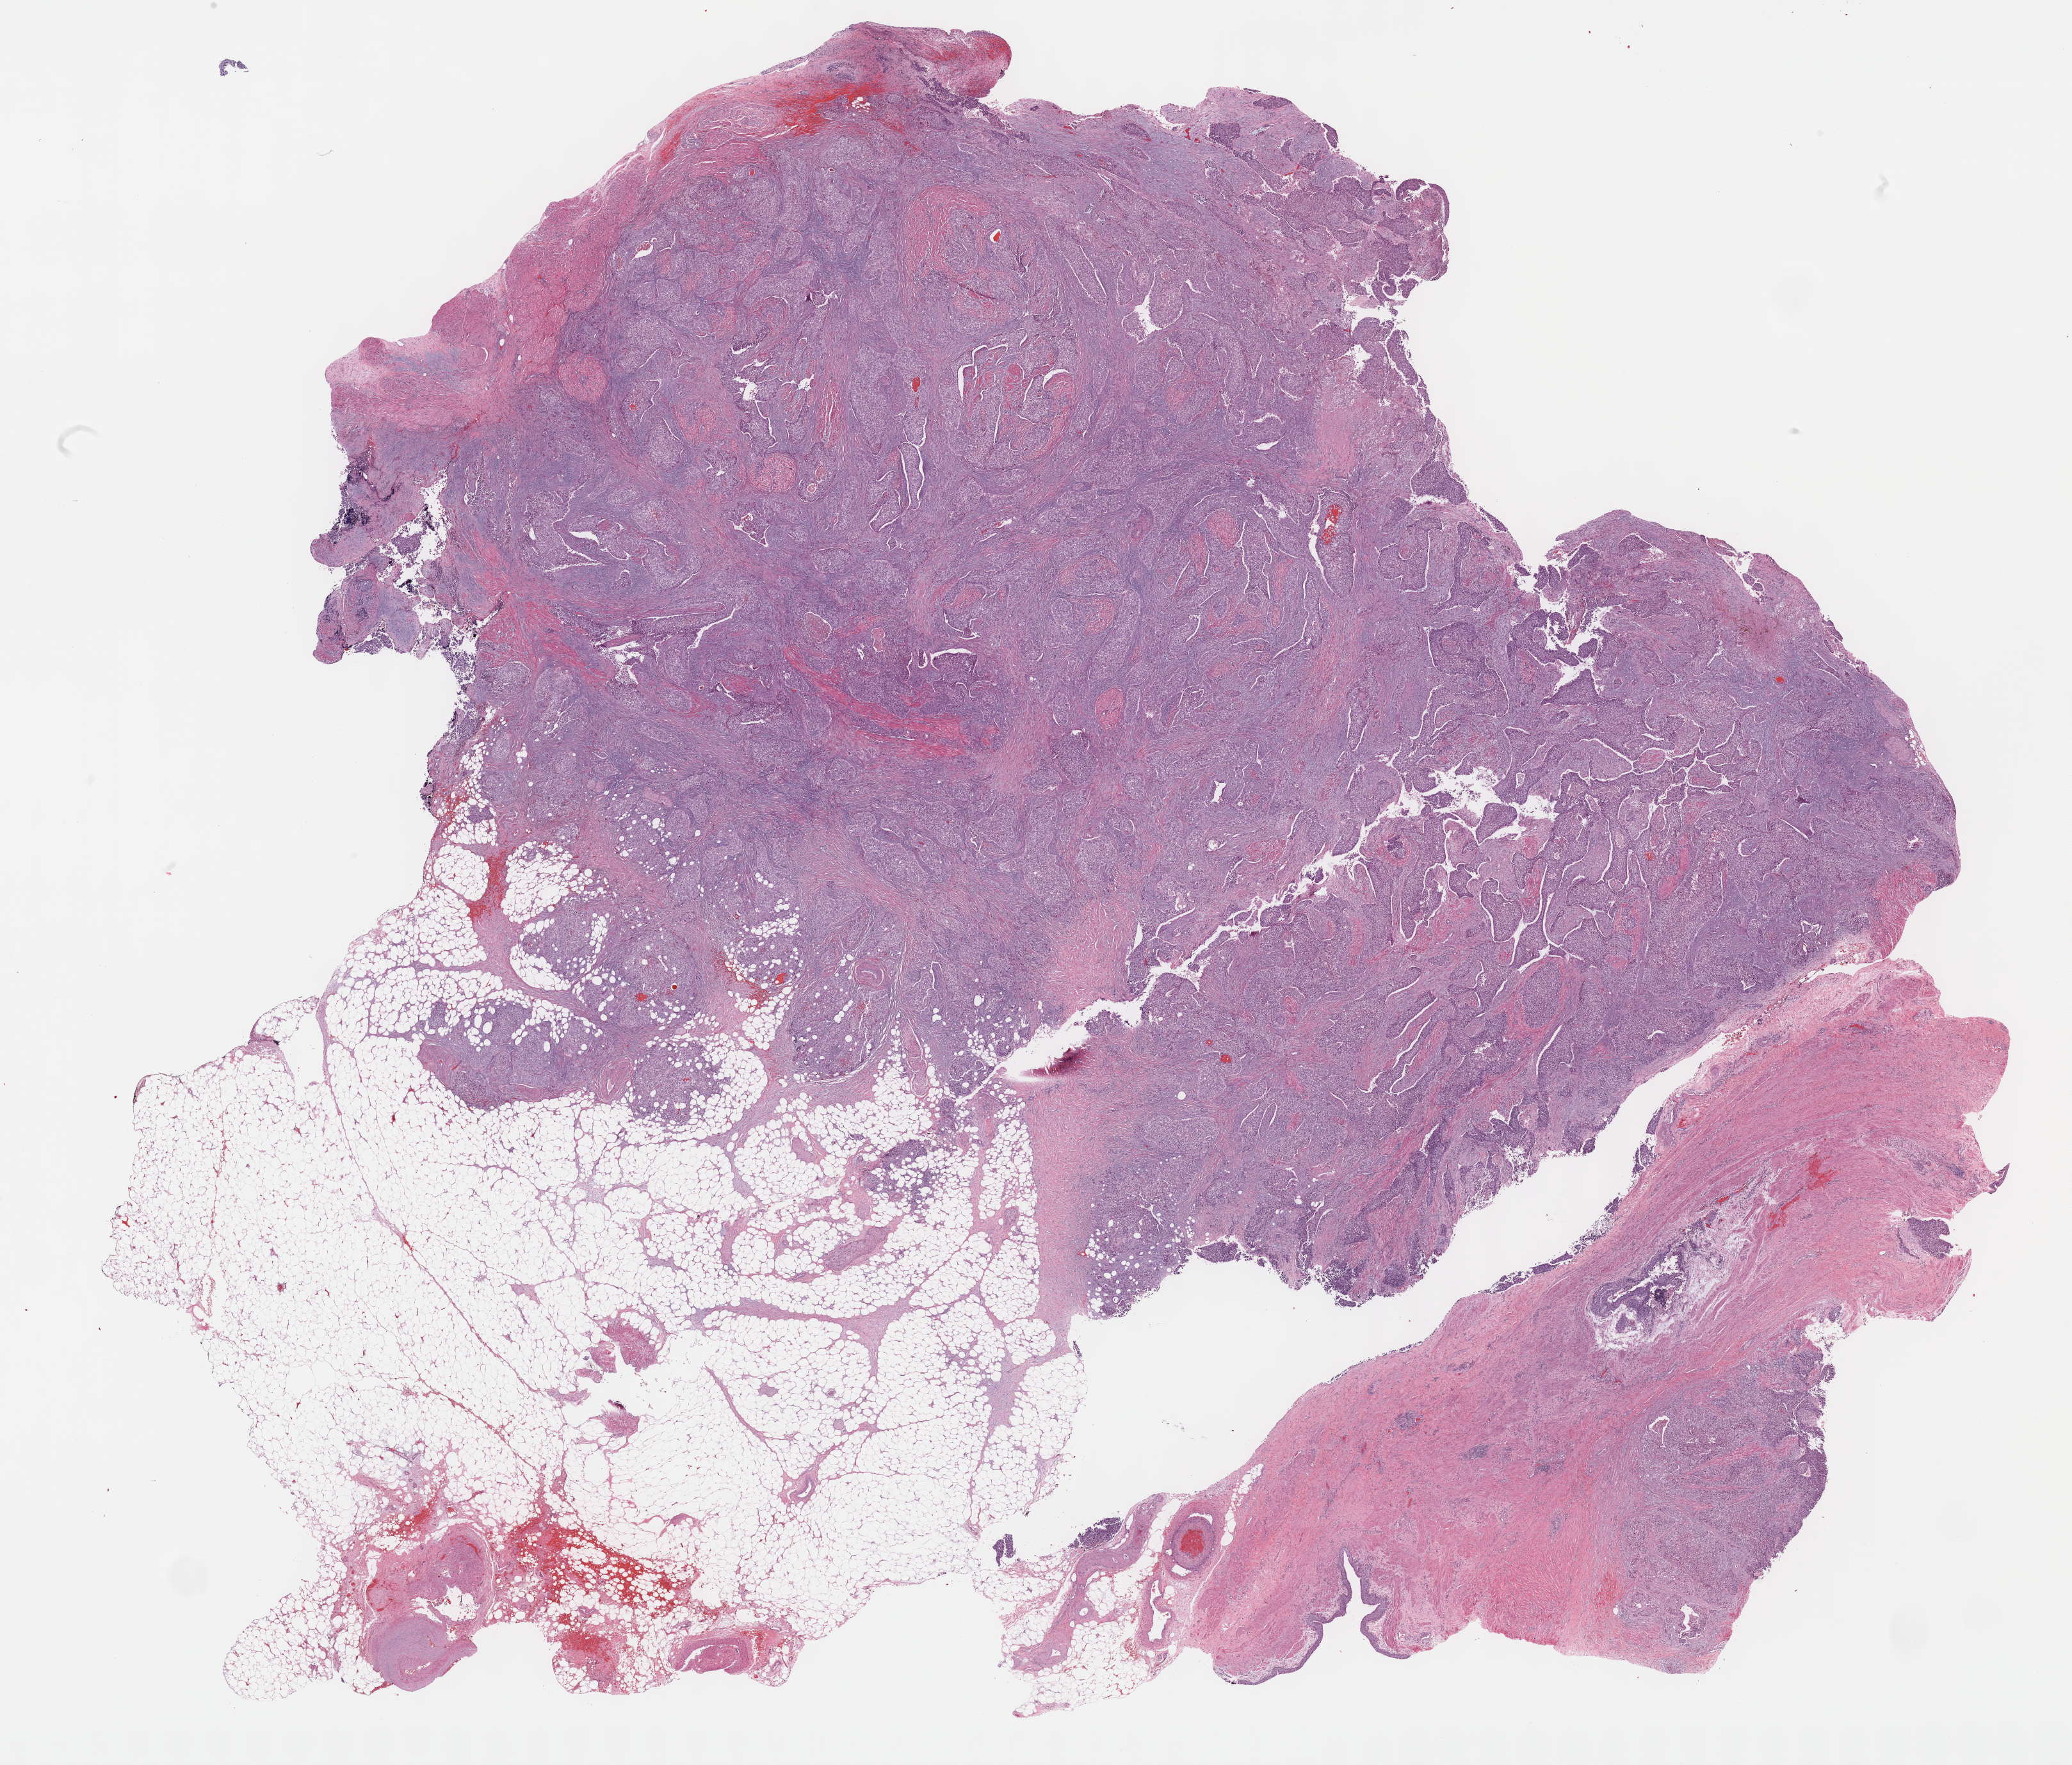
Digitized H&E tissue section (whole slide) — whole scanned area (about 26.2 x 22.3 mm, acquisition: 40x scan) shown as a low-resolution overview, formalin-fixed paraffin-embedded (FFPE) diagnostic section, primary tumour sample from the bladder. Male, age 78 years at initial diagnosis. Histologic grade: high grade.
AJCC pathologic stage: III (5th edition). Pathologic diagnosis: Papillary transitional cell carcinoma. TNM: T3b N0 MX. Lymph nodes positive (case pathology): 0 of 13 examined.